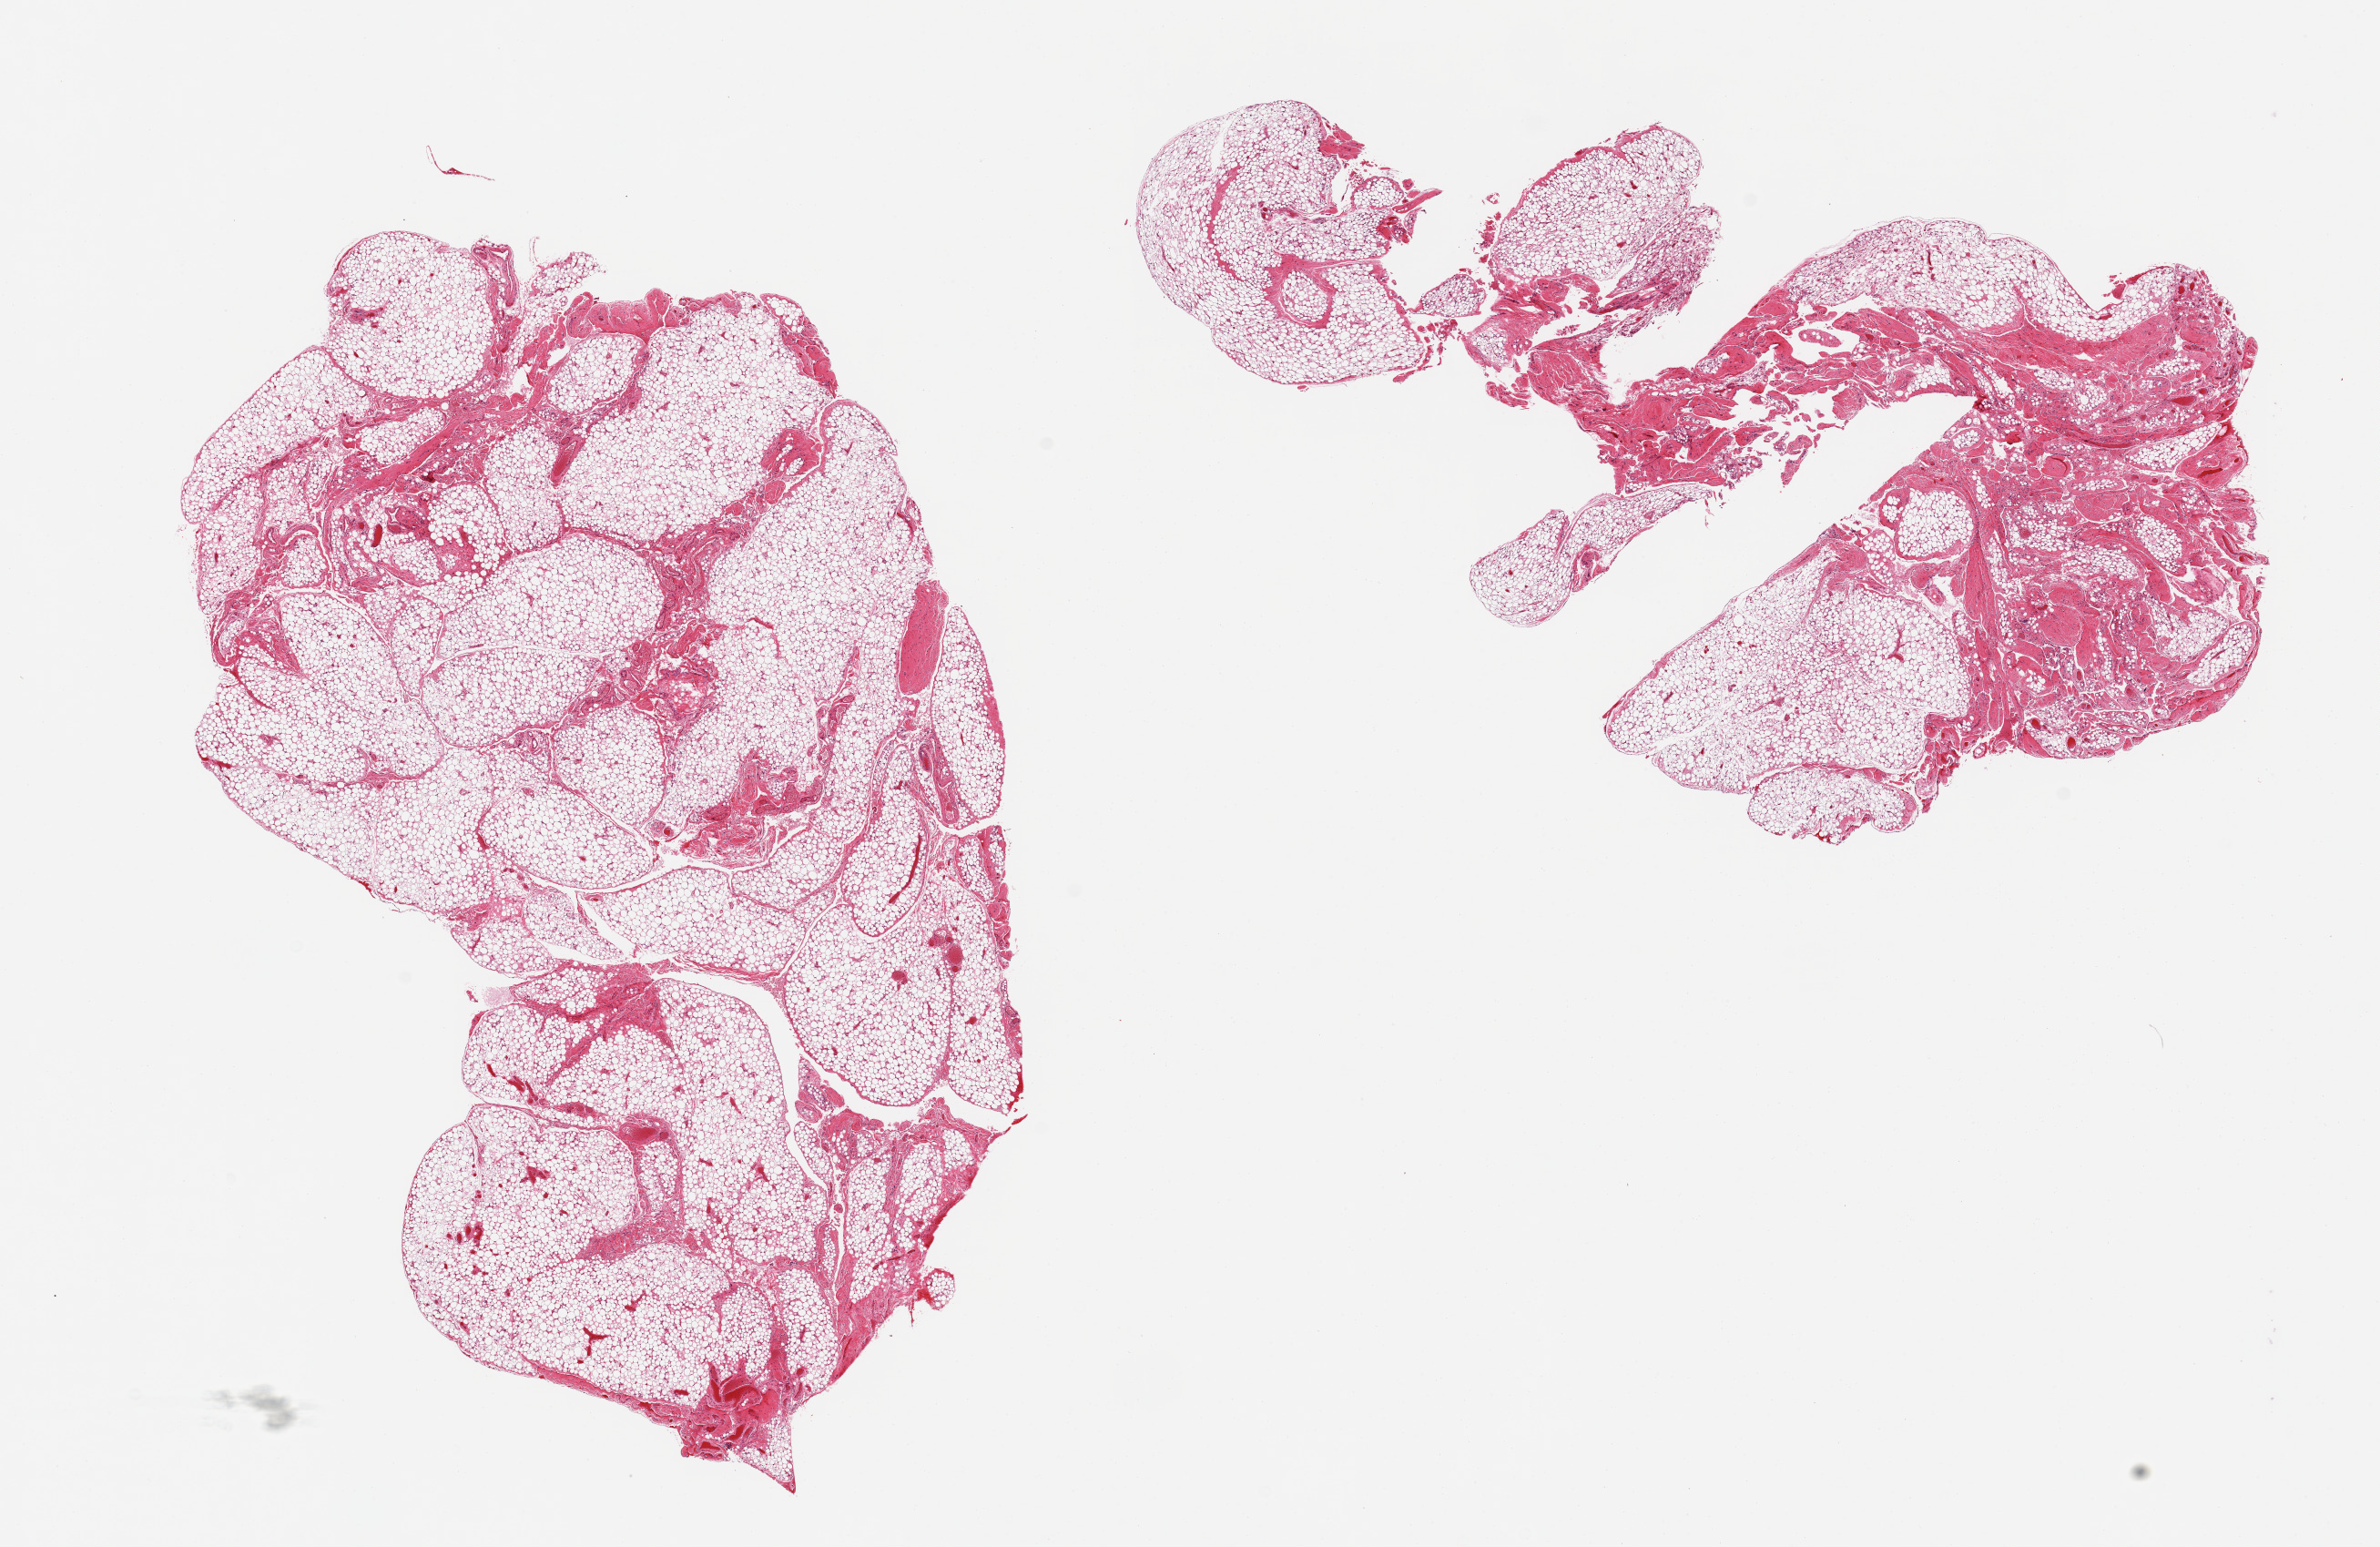
Digitized haematoxylin and eosin-stained section, brightfield — low-resolution overview of the scanned area, about 20.7 x 13.4 mm, PAXgene-fixed paraffin-embedded (PFPE) section, target tissue: omentum, tissue donor sample. Donor sex: male.
- reviewer comment on this tissue sample: 2 pieces; 15% and 30% of fibrovascular and smooth muscle tissue